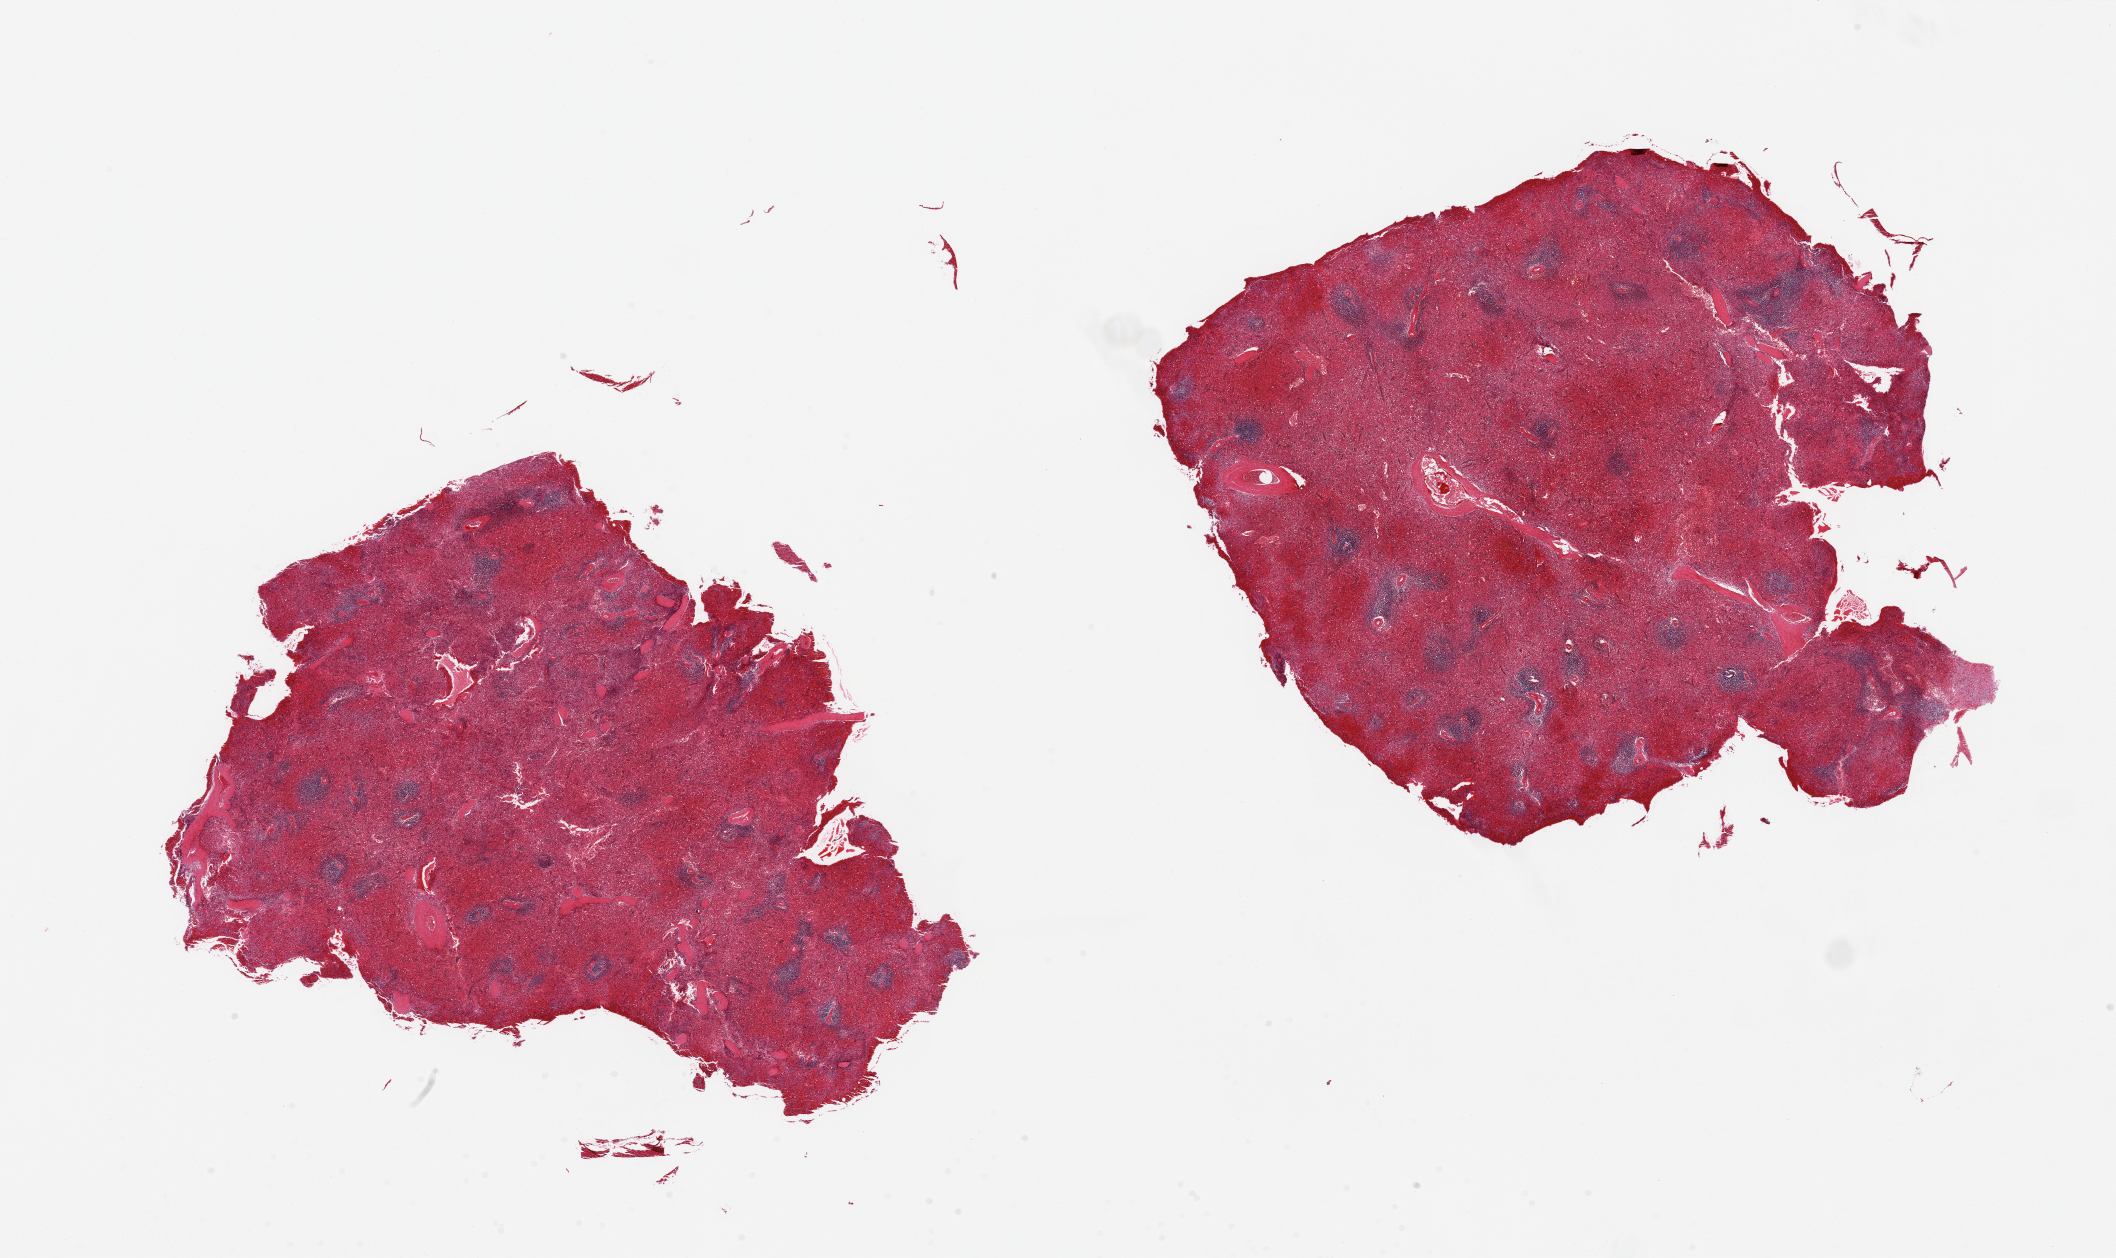
H&E whole-slide image — a low-resolution overview of the entire scanned area, about 33.5 x 19.9 mm; PAXgene-fixed, paraffin-embedded tissue; section of spleen (target tissue); tissue donor sample. Donor: male.
Review note (as recorded): 2 pieces, congested.